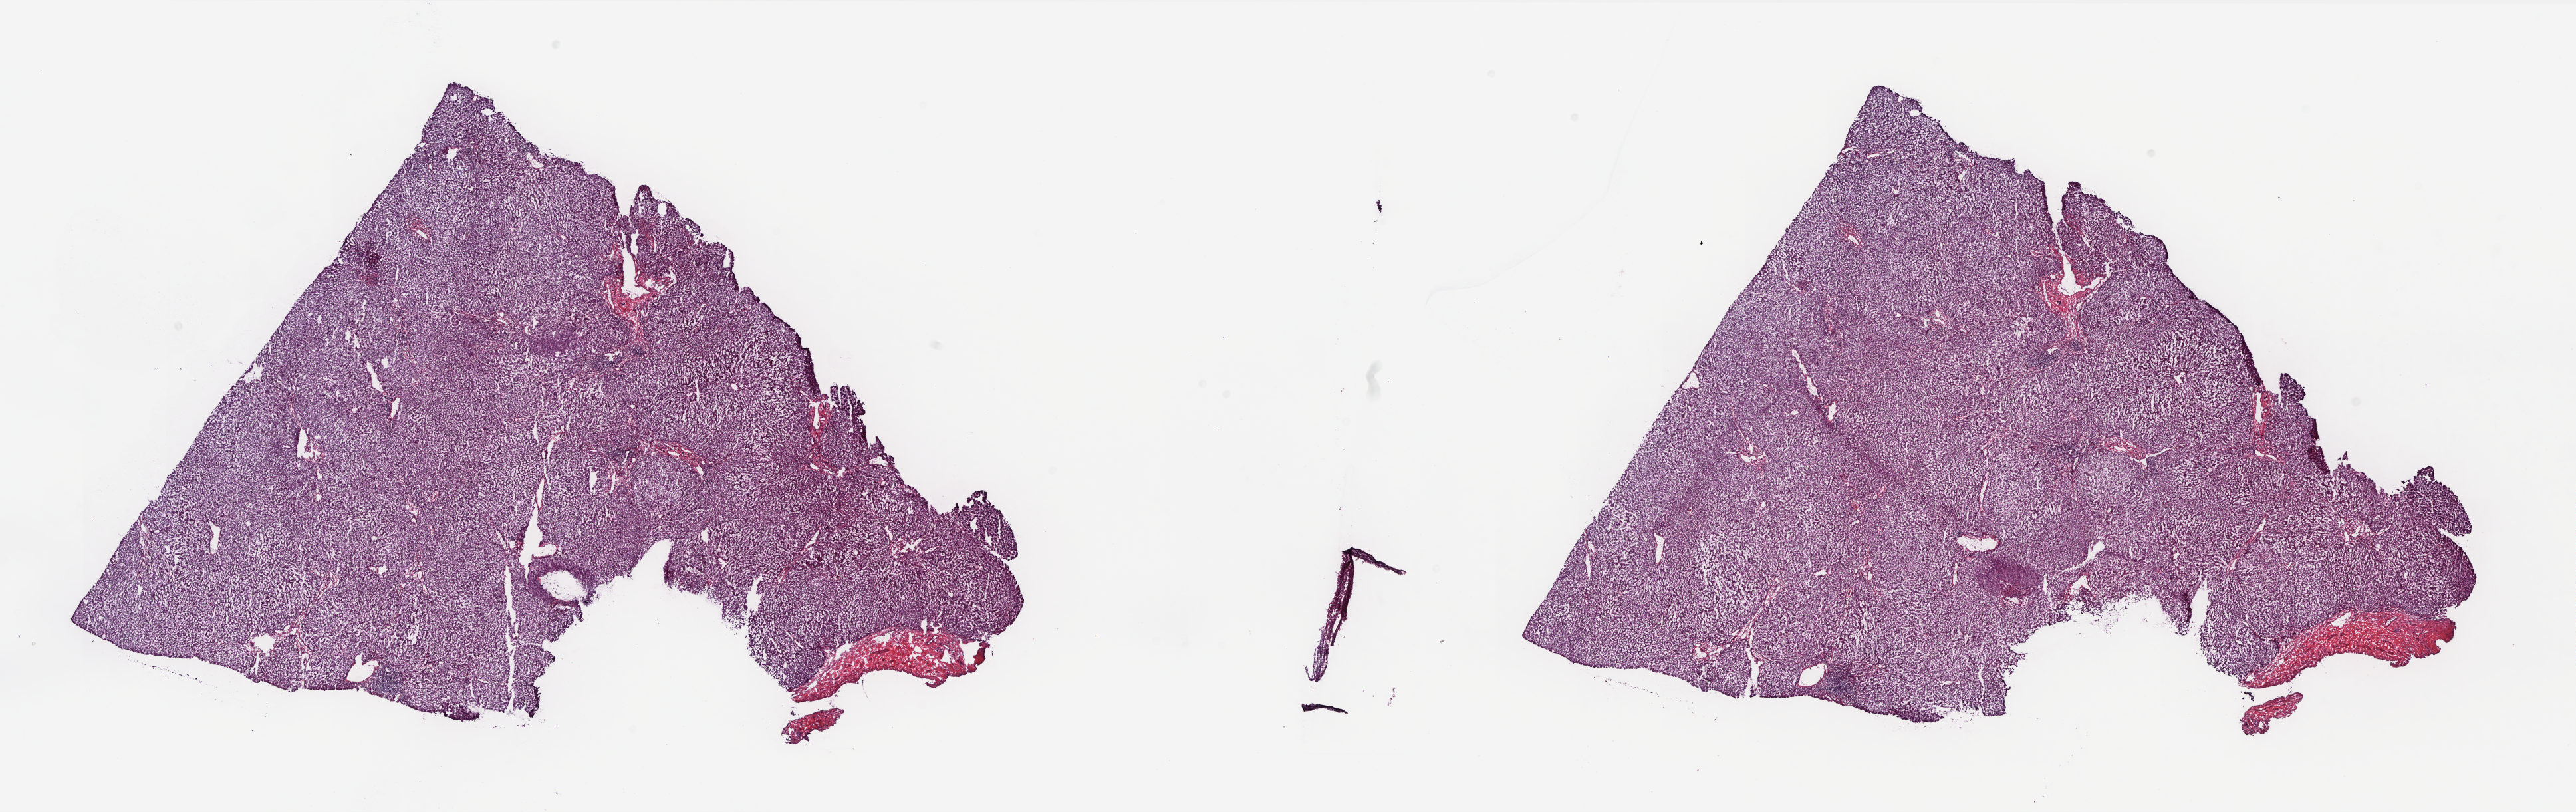
Digitized H&E tissue section (whole slide) — a low-resolution overview of the entire scanned area, about 30.9 x 9.8 mm (slide scanned at 20x); frozen section from the top of the tissue portion; sample: solid tissue normal (non-tumour tissue), liver. Male, age 53 years at initial diagnosis. Composition of this section per pathologist review: tumour cells 0%, tumour nuclei 0%, normal cells 100%, stromal cells 0%, necrosis 0%. Inflammatory infiltration, as recorded: lymphocyte infiltration 0%, monocyte infiltration 0%, neutrophil infiltration 0%.
- this section: solid tissue normal (non-tumour) sample from the same patient
- patient diagnosis: Hepatocellular carcinoma, NOS